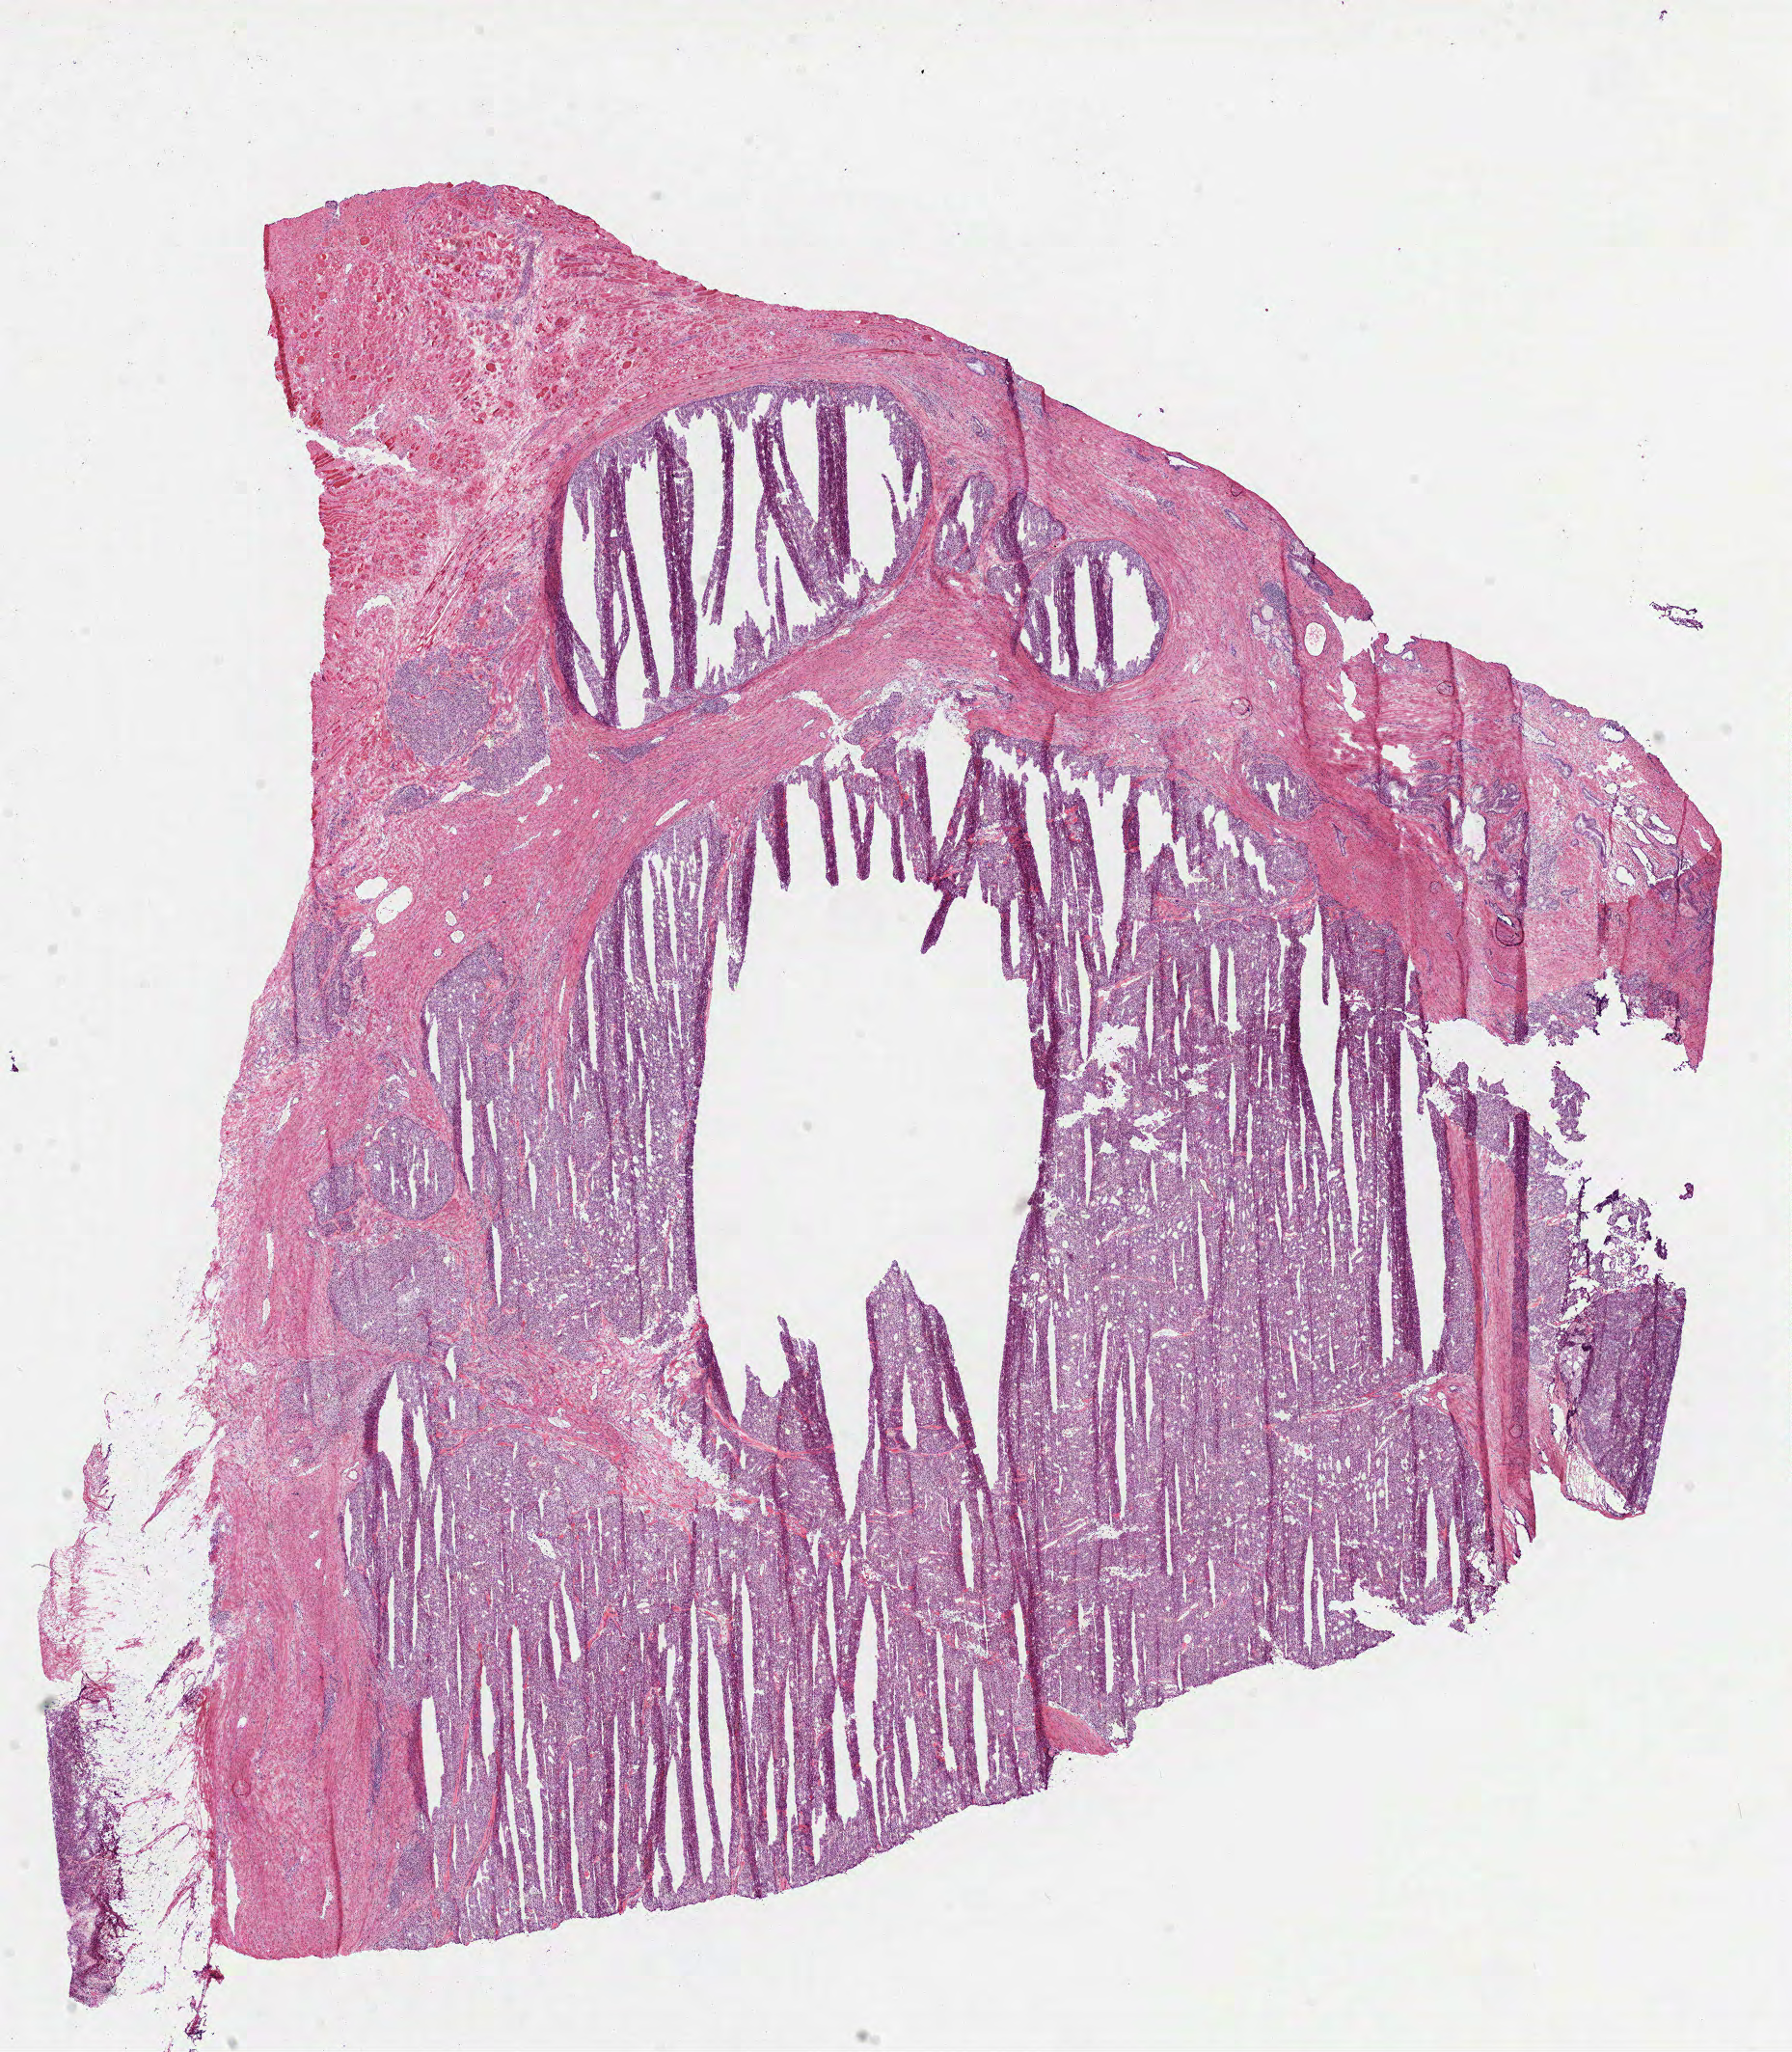
Whole-slide histology image, H&E — whole scanned area (about 15.0 x 17.2 mm) shown as a low-resolution overview; frozen section; prostate, primary tumour sample. Patient: male, age at initial diagnosis 66 years. Gleason score: 7 (4+3). Composition of this section per pathologist review: tumour cells 80%, tumour nuclei 90%, normal cells 5%, stromal cells 15%, necrosis 0%. Infiltration values recorded for this section: lymphocyte infiltration 0%, monocyte infiltration 0%, neutrophil infiltration 0%.
- laterality: bilateral
- histologic diagnosis: Acinar cell carcinoma (prostate gland)
- lymph nodes positive (case pathology): 0 of 14 examined